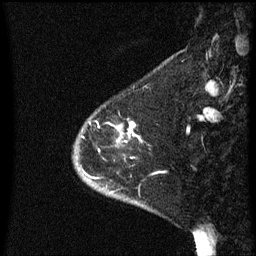
Breast MRI (dynamic contrast-enhanced), one sagittal slice. Dynamic contrast-enhanced series, image 2 of 3 at this slice position (ordered by acquisition). 1.5 T. TE 4.2 ms, TR 8.4 ms. 2.3 mm slice thickness. 256 × 256 image matrix, field of view 200 × 200 mm. Patient: female, 46 years. Case-level facts recorded for this patient, not image findings: setting: breast cancer imaged before/during neoadjuvant chemotherapy; receptor status: HER2-positive.
Annotated regions visible in this slice (semi-automatically segmented with operator editing):
- analysis volume of interest (the breast-tissue region the enhancement analysis was run in; not a lesion): bounding box [x1, y1, x2, y2] px = [75, 120, 142, 187]
- tumour enhancement mask (voxels above the 70 % enhancement threshold inside the analysis volume of interest): [118, 126, 120, 131]